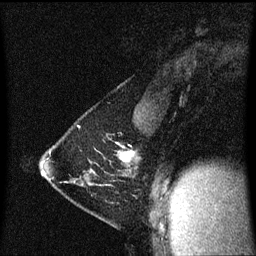
Breast MRI (dynamic contrast-enhanced), one sagittal slice. Position 36 of 60 along the scan axis. Dynamic contrast-enhanced series, image 2 of 3 at this slice position (ordered by acquisition). 1.5 T. TE 4.2 ms, TR 8.4 ms. 256 × 256 image matrix. Female patient, age 40 years. Case-level facts recorded for this patient, not image findings: setting: breast cancer imaged before/during neoadjuvant chemotherapy; receptor status: triple-negative.
Structures marked on this image (semi-automatically segmented with operator editing):
- analysis volume of interest (the breast-tissue region the enhancement analysis was run in; not a lesion): bounding box <41,142,134,185> (left, top, right, bottom; pixels)
- tumour enhancement mask (voxels above the 70 % enhancement threshold inside the analysis volume of interest): <123,156,129,159>